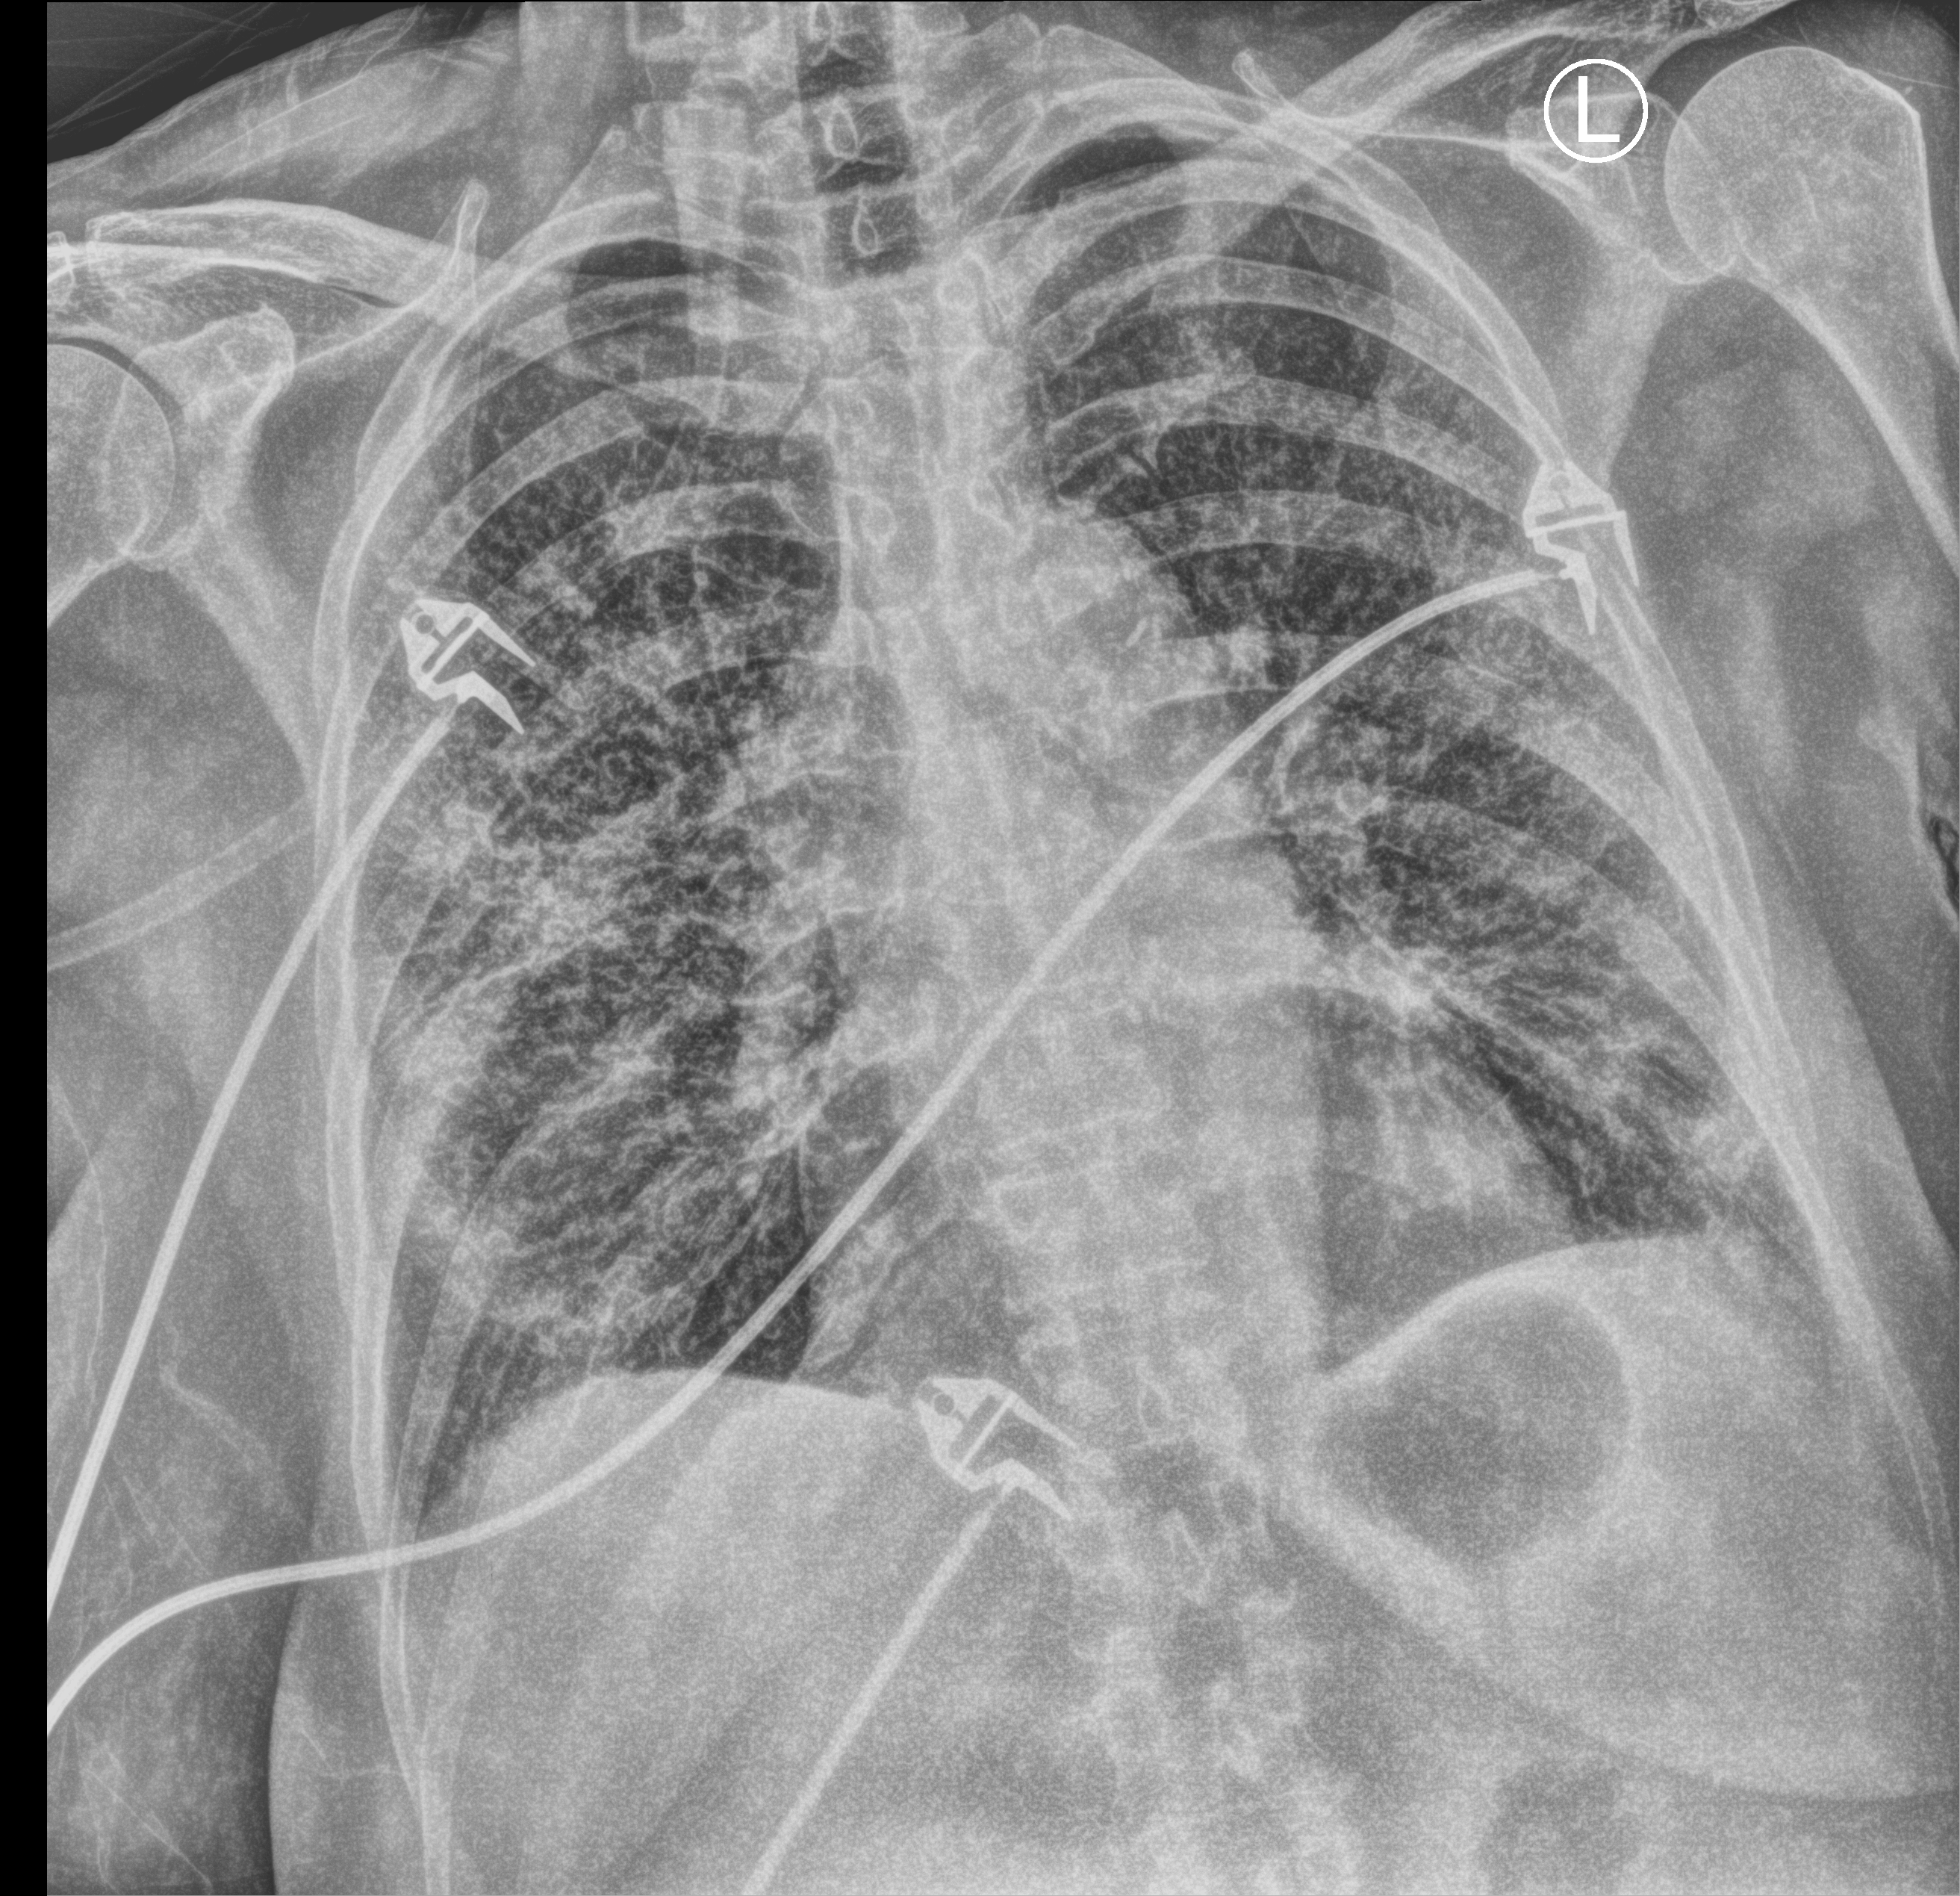
Portable chest radiograph, anteroposterior (AP) projection. Female patient hospitalised with COVID-19, age 60–74 years.
Hospital-stay facts (about this admission, not read from this image; timing relative to this image not recorded):
- chronic kidney disease (admission record): no
- mechanically ventilated during this hospital stay: yes